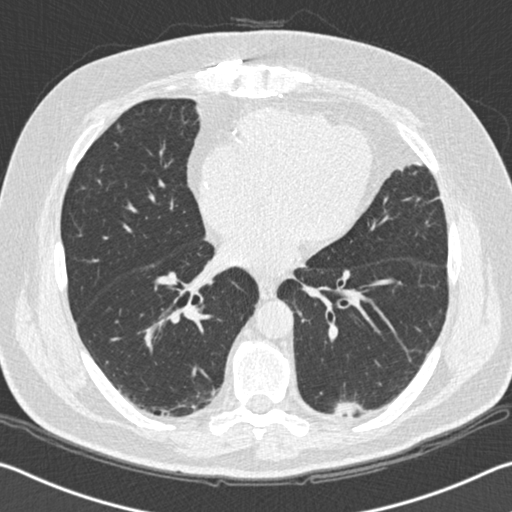
Axial slice from a low-dose chest CT screening exam. Second annual screen. Lung window (W 1500 / L -600 HU). Standard (soft-tissue) reconstruction kernel (B30f). Slice 94 of 172 in the series. Male, age 65 years at enrolment. Former smoker at enrolment.
• Expert-annotated lung lesion, bounding box [x1, y1, x2, y2] px = [324, 387, 385, 435].
• Screening reader's record for this exam (one nodule recorded; not confirmed to be the boxed lesion): non-calcified nodule or mass ≥4 mm, left lower lobe, 19 × 11 mm, spiculated (stellate) margins, soft tissue attenuation, pre-existing on the prior screen: yes; interval growth: yes.
• Official screen result: positive, change unspecified: nodule(s) >= 4 mm or enlarging nodule(s), mass(es), or other non-specific abnormalities suspicious for lung cancer.
• Participant outcome: lung cancer diagnosed 179 days after this screen — squamous cell carcinoma, NOS, left lower lobe, moderately differentiated (G2), stage IA (AJCC 6th edition), 20 mm at pathology.